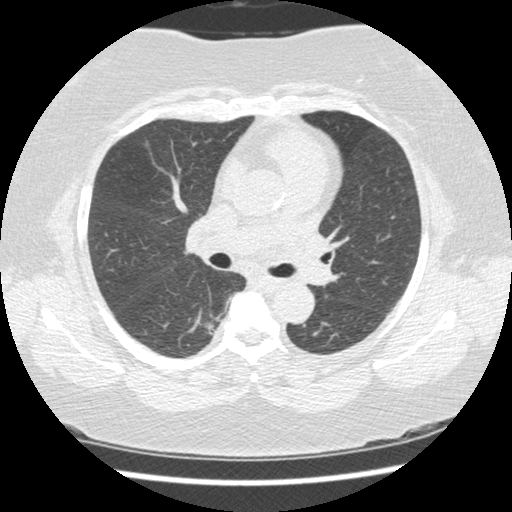
Chest CT (low-dose screening protocol), one axial image, second annual screen, lung window (W 1500 / L -600 HU), 1.25 mm slice thickness, standard (soft-tissue) reconstruction kernel (STANDARD), 512 × 512 image matrix, field of view 331 × 331 mm. Female participant, aged 58 years at enrolment. Current smoker at enrolment.
Lesion marked by an expert reader, bounding box (x1, y1, x2, y2) in pixels: (188, 309, 228, 348). The exam's reader record, not a measurement of the box and not confirmed to be the same lesion: non-calcified nodule or mass ≥4 mm, right lower lobe, 15 × 15 mm, spiculated (stellate) margins, soft tissue attenuation, pre-existing on the prior screen: yes; interval growth: yes. Official screen result: positive, change unspecified: nodule(s) >= 4 mm or enlarging nodule(s), mass(es), or other non-specific abnormalities suspicious for lung cancer.